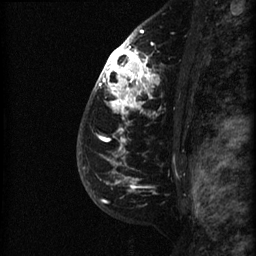
Breast MRI (dynamic contrast-enhanced), one sagittal slice. Slice 48 of 60 in the series (ordered by position). Dynamic contrast-enhanced series, image 2 of 3 at this slice position (ordered by acquisition). 1.5 T. TE 4.2 ms, TR 22.7 ms. 256 × 256 image matrix, field of view 180 × 180 mm. Female patient, age 48 years. Case-level facts recorded for this patient, not image findings: setting: breast cancer imaged before/during neoadjuvant chemotherapy; receptor status: triple-negative.
Annotated regions visible in this slice (semi-automatically segmented with operator editing):
- analysis volume of interest (the breast-tissue region the enhancement analysis was run in; not a lesion): box from (x=89, y=27) to (x=190, y=180) px
- tumour enhancement mask (voxels above the 90 % enhancement threshold inside the analysis volume of interest): (x=99, y=30)–(x=157, y=180)